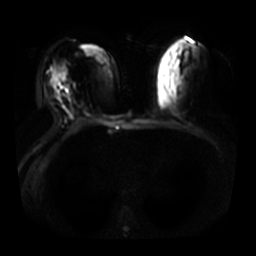
Breast MRI, one axial slice; position 15 of 31 along the scan axis; diffusion-weighted series; image 2 of 4 stored at this slice position (different b-values; order by instance number); 3 T; 256 × 256 image matrix. Female patient.
Annotated regions visible in this slice (outlined manually by an expert reader):
- tumour on diffusion-weighted imaging: box from (x=58, y=82) to (x=63, y=89) px